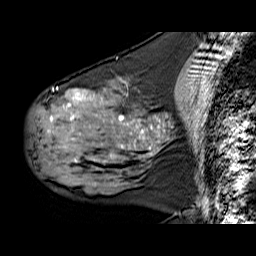
Breast MRI (dynamic contrast-enhanced), one sagittal slice. Slice 26 of 60 in the series (ordered by position). Dynamic contrast-enhanced series, time point 2 of 6 at this slice position (early post-contrast). 1.5 T. TE 6.3 ms, TR 32.9 ms. 4 mm slice thickness. 256 × 256 image matrix, field of view 200 × 200 mm. Female patient. From the clinical record (not read from this slice): setting: breast cancer imaged before/during neoadjuvant chemotherapy; receptor status: HER2-positive.
Annotated regions visible in this slice (semi-automatic segmentation, software-assisted and operator-edited):
- analysis volume of interest (the breast-tissue region the enhancement analysis was run in; not a lesion): bounding box [x1, y1, x2, y2] px = [30, 78, 169, 180]
- tumour enhancement mask (voxels above the 100 % enhancement threshold inside the analysis volume of interest): [50, 92, 160, 149]